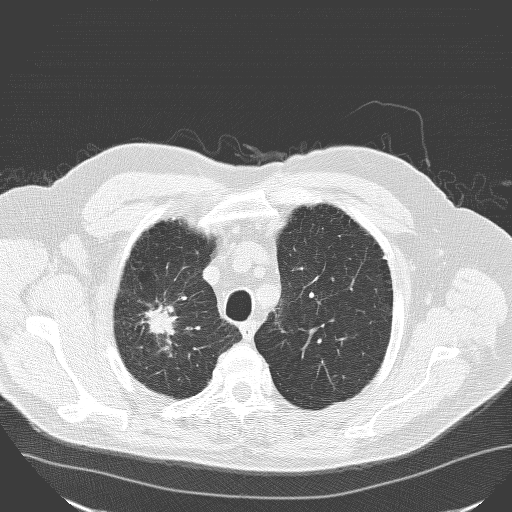
Low-dose screening chest CT, one axial slice. Slice 133 of 160 in the series (ordered by position). 120 kVp. Lung window (W 1500 / L -600 HU). 3.2 mm slice thickness. 512 × 512 image matrix.
Outlined on this slice (outlined manually by an expert reader):
- lesion 1 (tumor, upper lobe of right lung): bounding box [x1, y1, x2, y2] px = [145, 304, 176, 337]